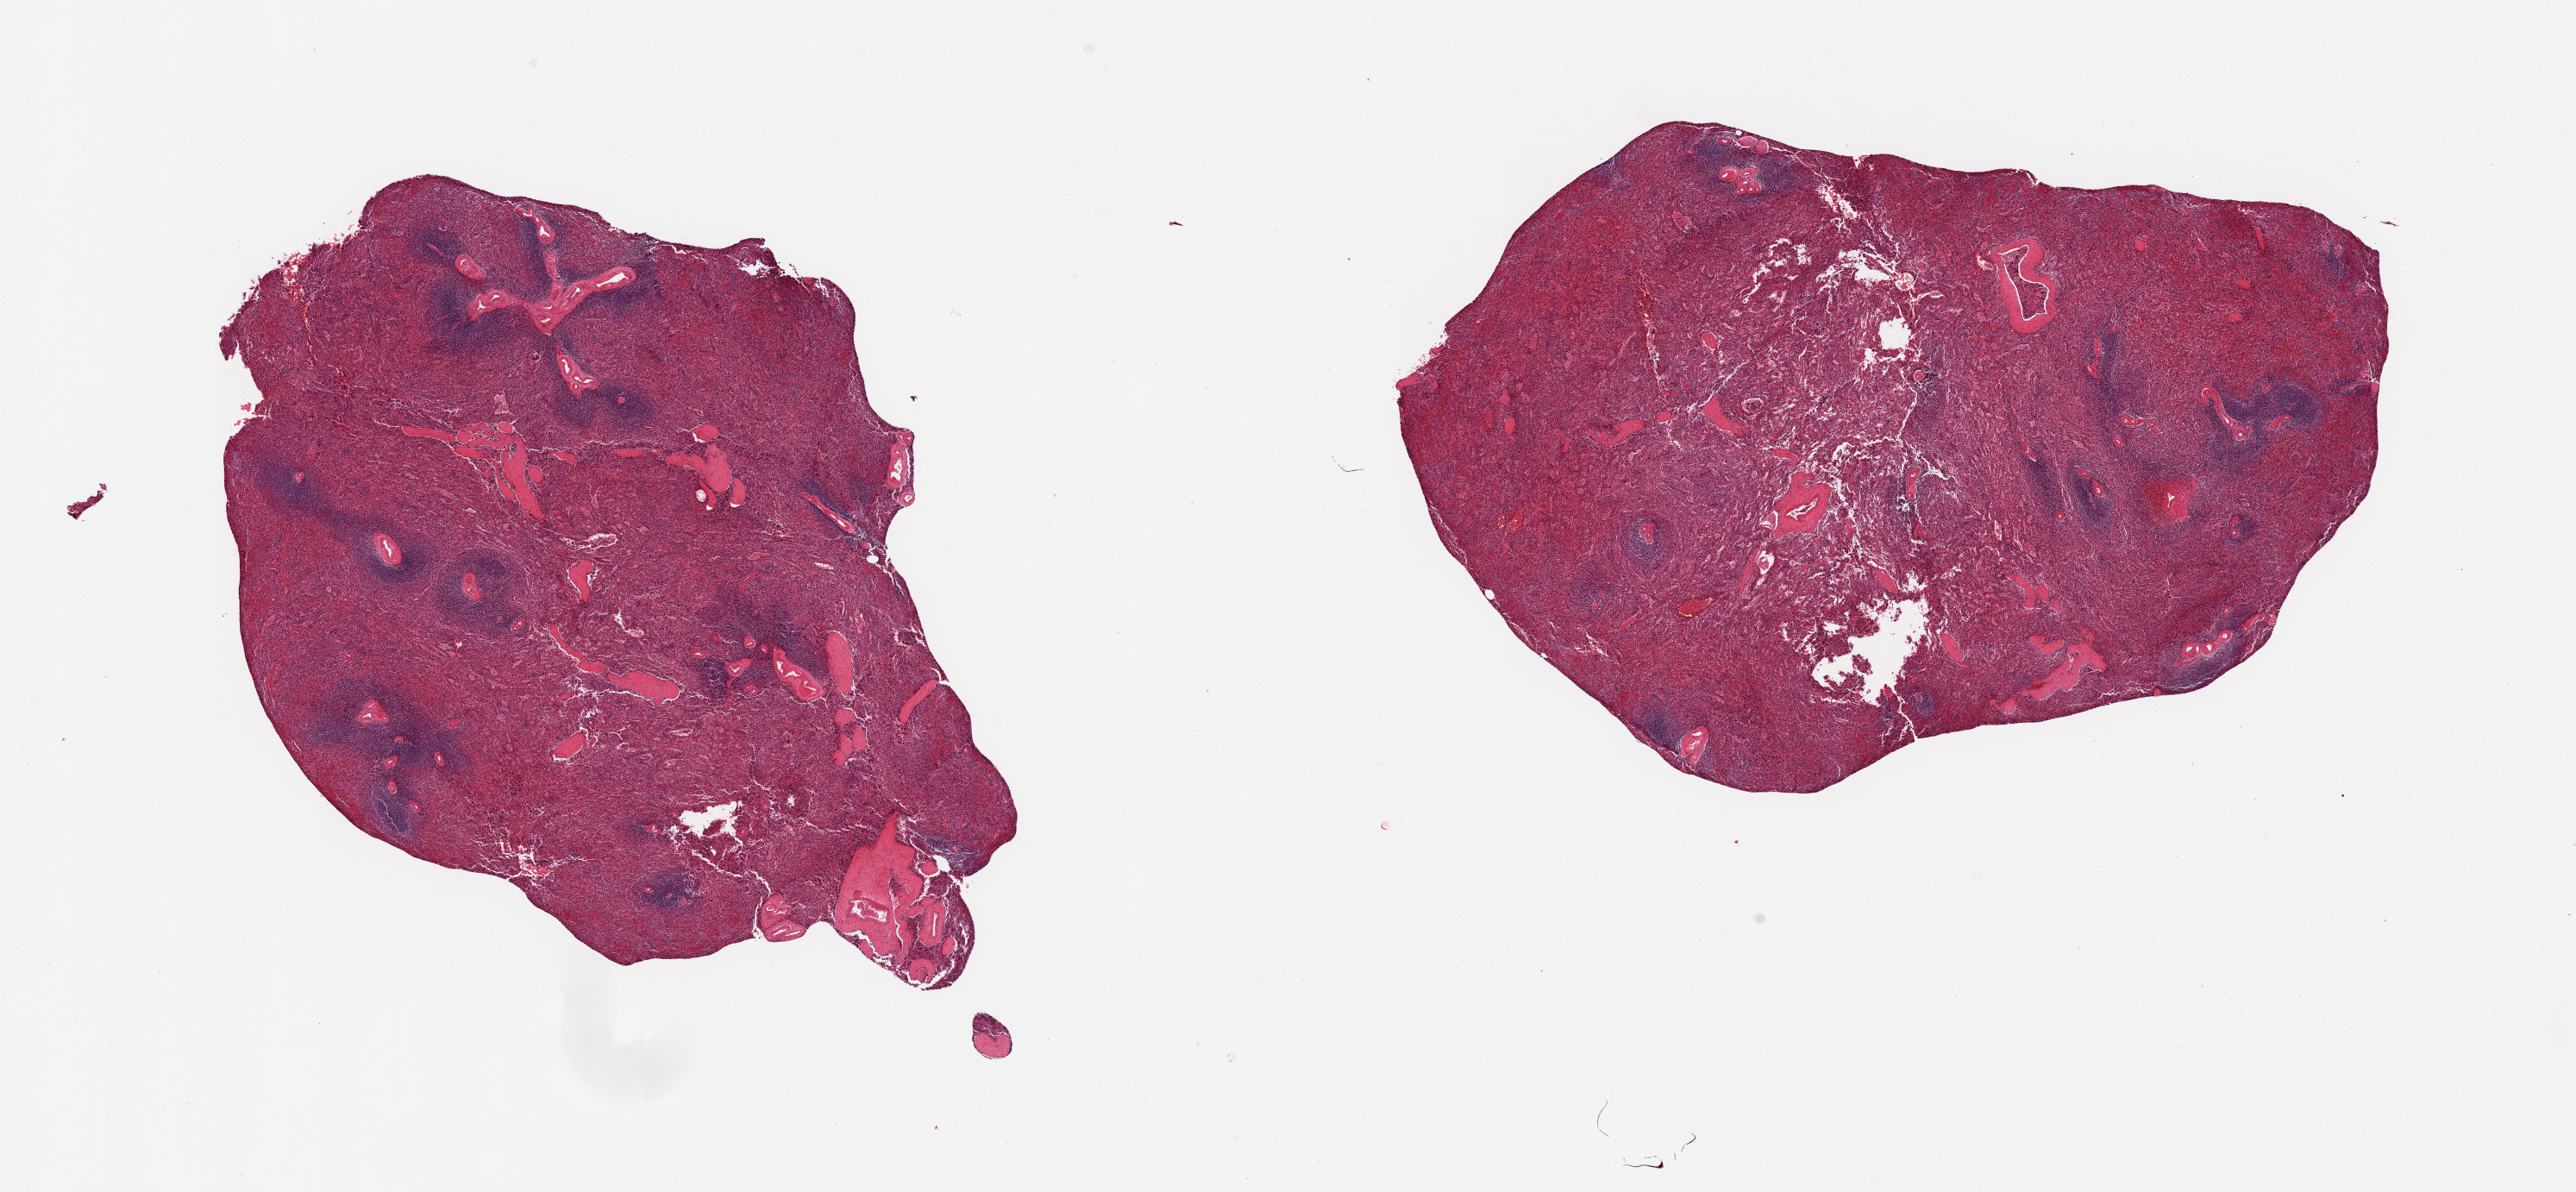
Haematoxylin and eosin whole-slide image — shown as a low-resolution overview of the whole scanned area (about 23.6 x 10.9 mm). PAXgene-fixed paraffin-embedded (PFPE) section. Target tissue: spleen. Donor tissue sample. Donor: female.
Reviewer comment on this tissue sample: 2 pieces; congested.